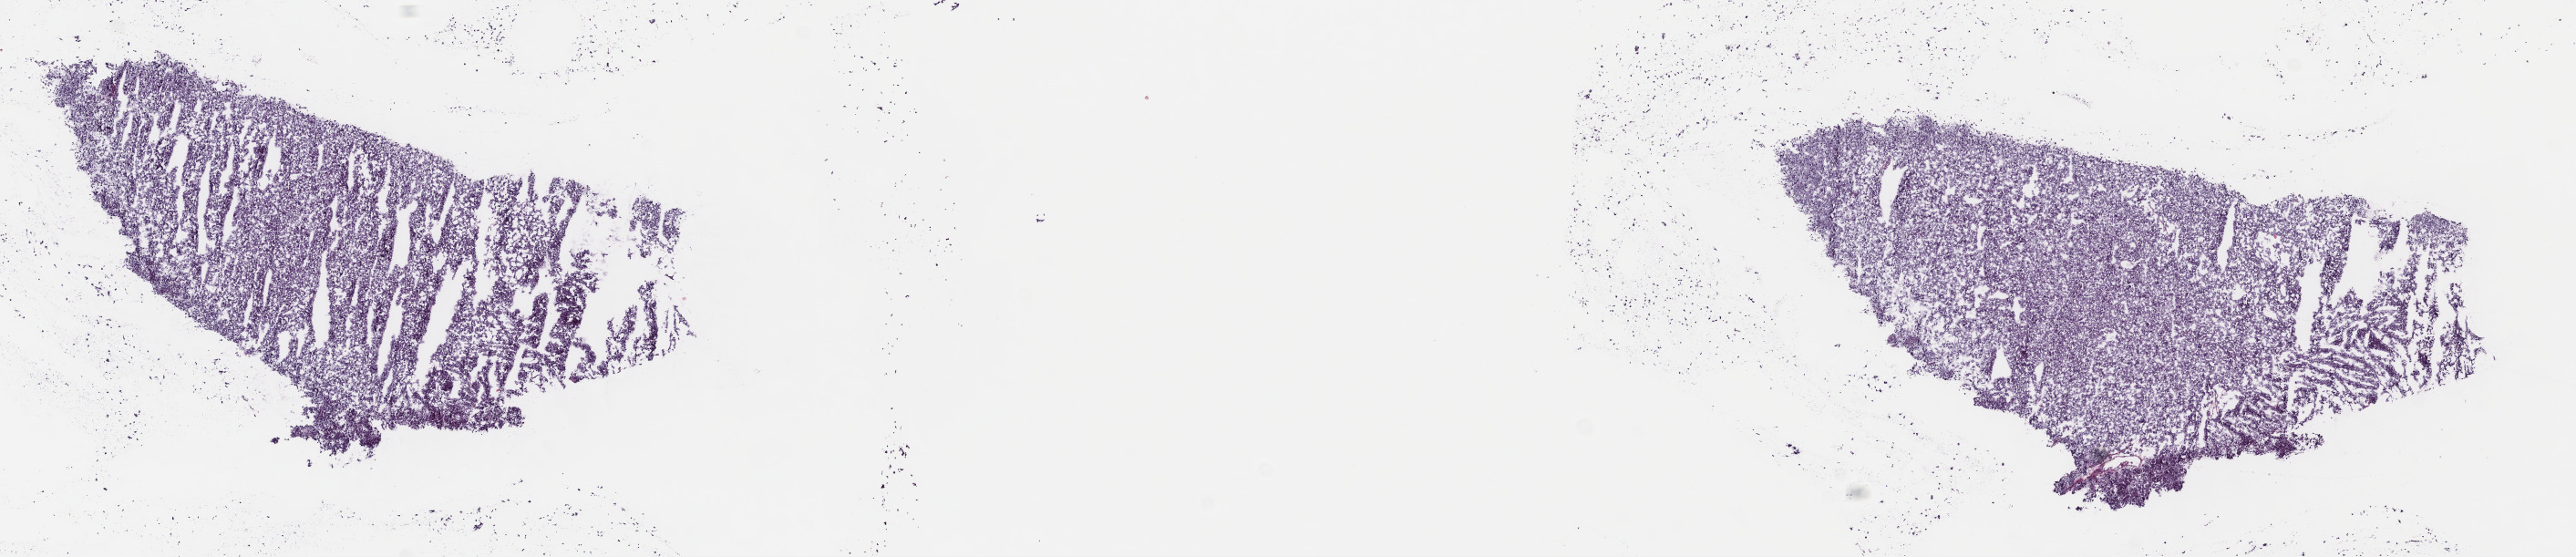
H&E whole-slide image, low-resolution overview of the scanned area, about 22.2 x 4.8 mm; frozen section; adrenal gland, primary tumour sample. Female patient; age at initial diagnosis 69 years.
Histologic diagnosis: Pheochromocytoma, NOS.